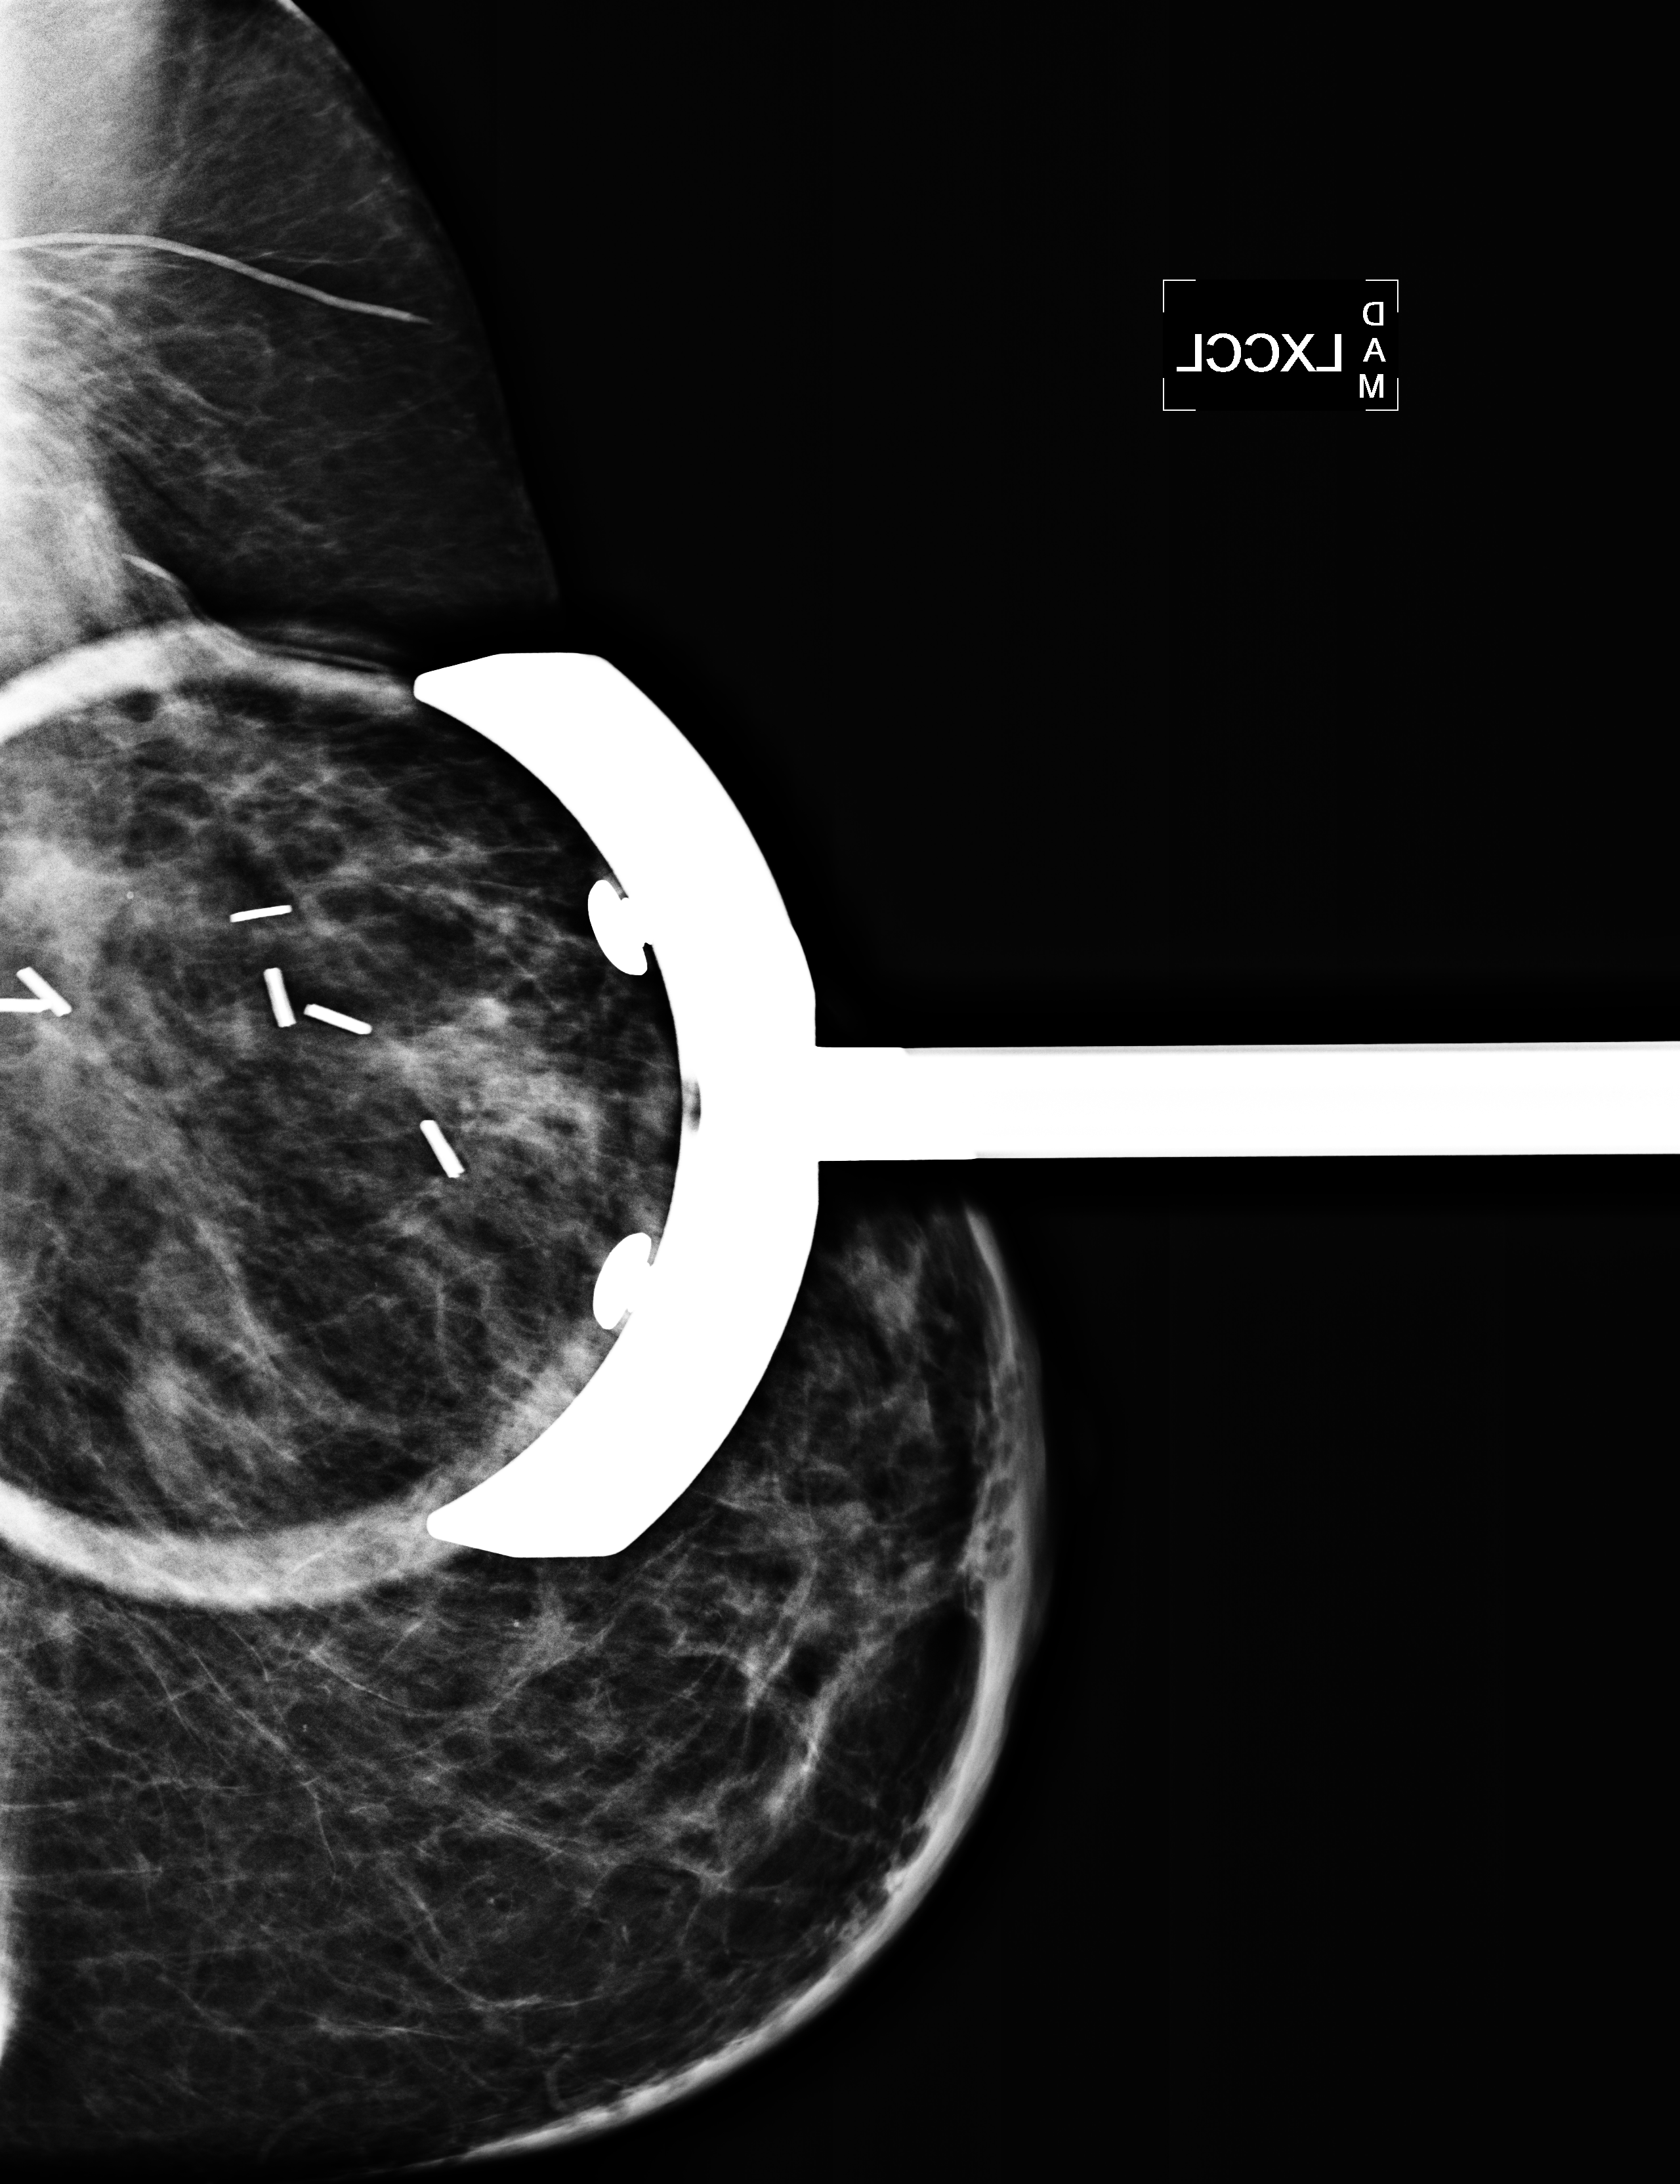
Mammogram, left breast, XCCL view; patient in her 50s.
Patient-level pathology facts (clinical record, not image findings): pathology diagnosis: Invasive ductal CA (left breast); receptor status (as recorded): ER pos, PR pos (weak), HER2 neg; pathology report notes: re-bx [date] was scar tissue from RT rx.